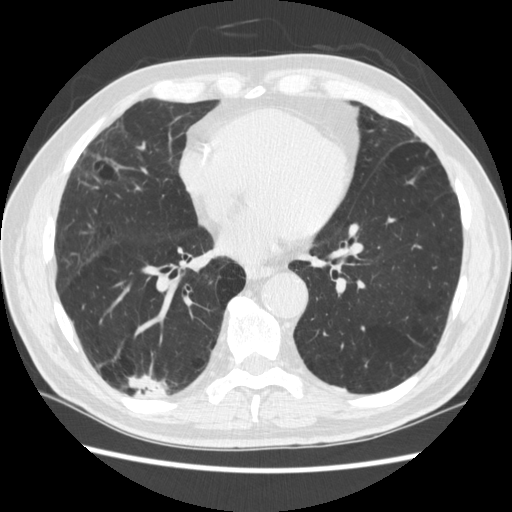
Low-dose screening chest CT, one axial slice; position 114 of 266 along the scan axis; reconstruction kernel STANDARD; lung window (W 1500 / L -600 HU); 1.25 mm slice thickness; 512 × 512 image matrix, field of view 360 × 360 mm.
Annotated regions visible in this slice (expert manual segmentation):
- lesion 1 (tumor, upper lobe of right lung): bounding box (x1, y1, x2, y2) in pixels: (129, 376, 167, 399)